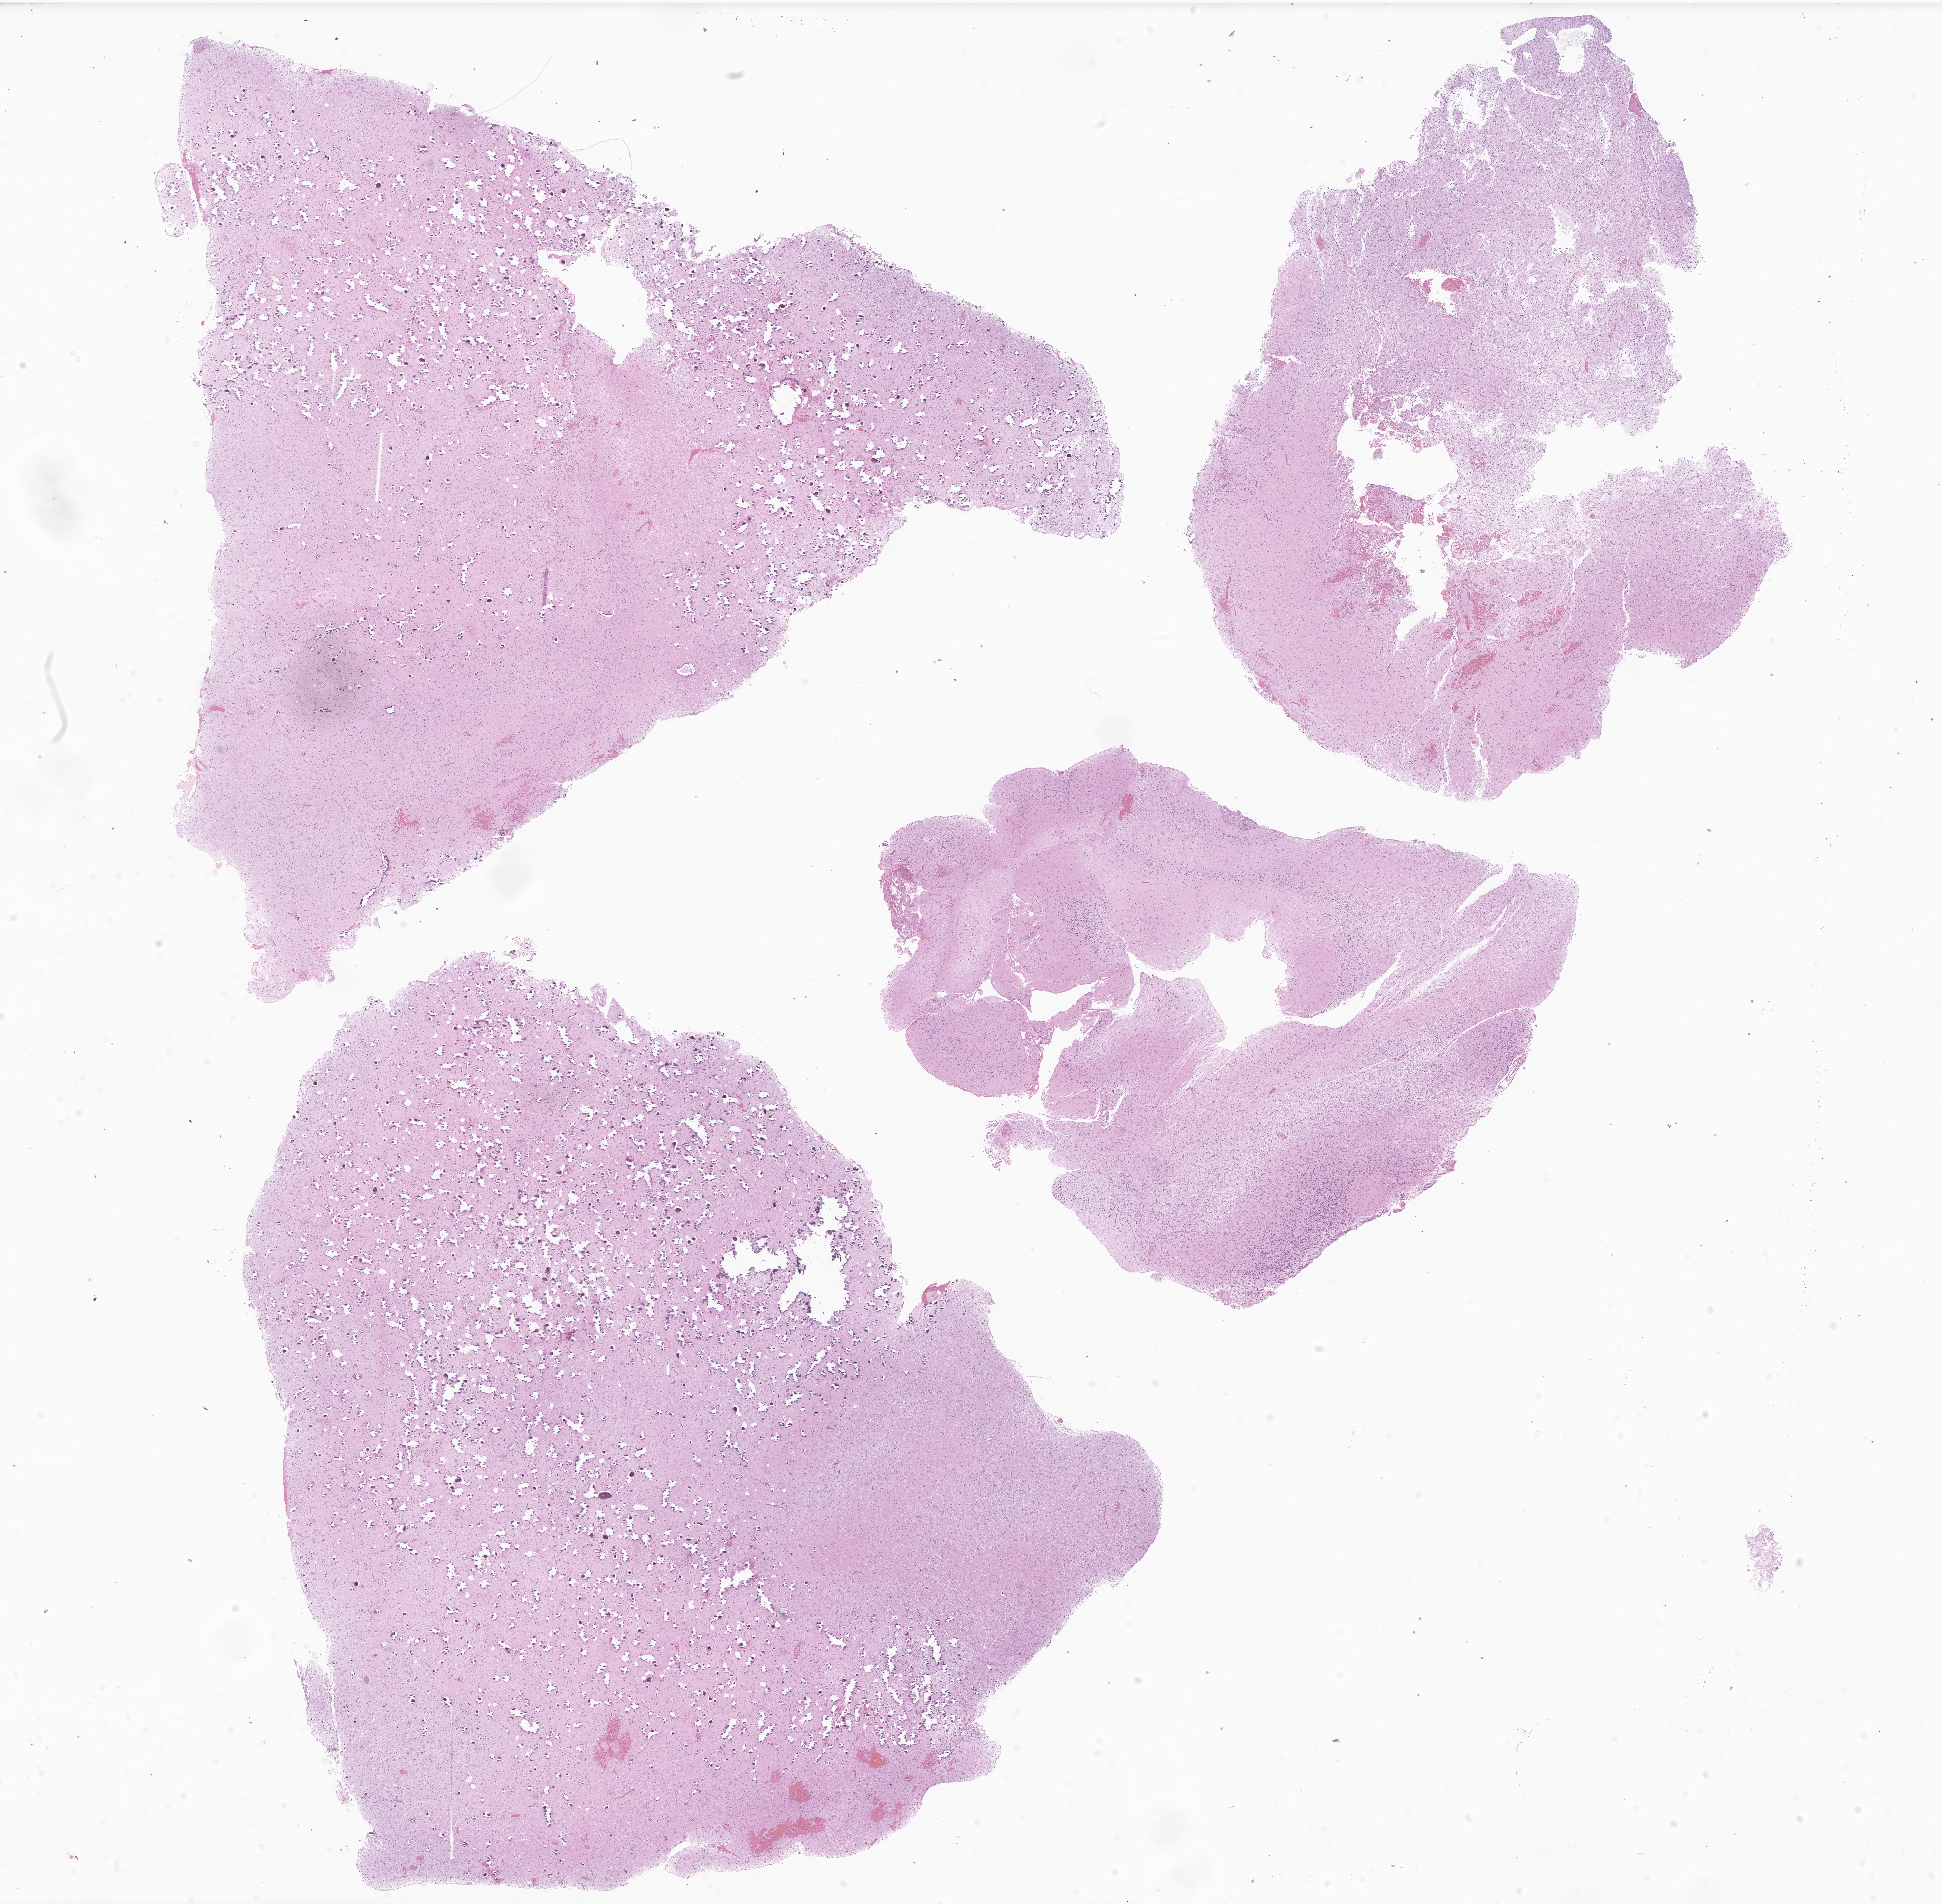
Digitized hematoxylin and eosin (H&E)-stained section of tumor tissue from the cerebellum, shown as a low-resolution overview of the whole scanned area (about 23.7 x 23.2 mm), FFPE section. Patient male; age 145 months (12 years 1 month).
Recorded diagnosis: Pilocytic astrocytoma.